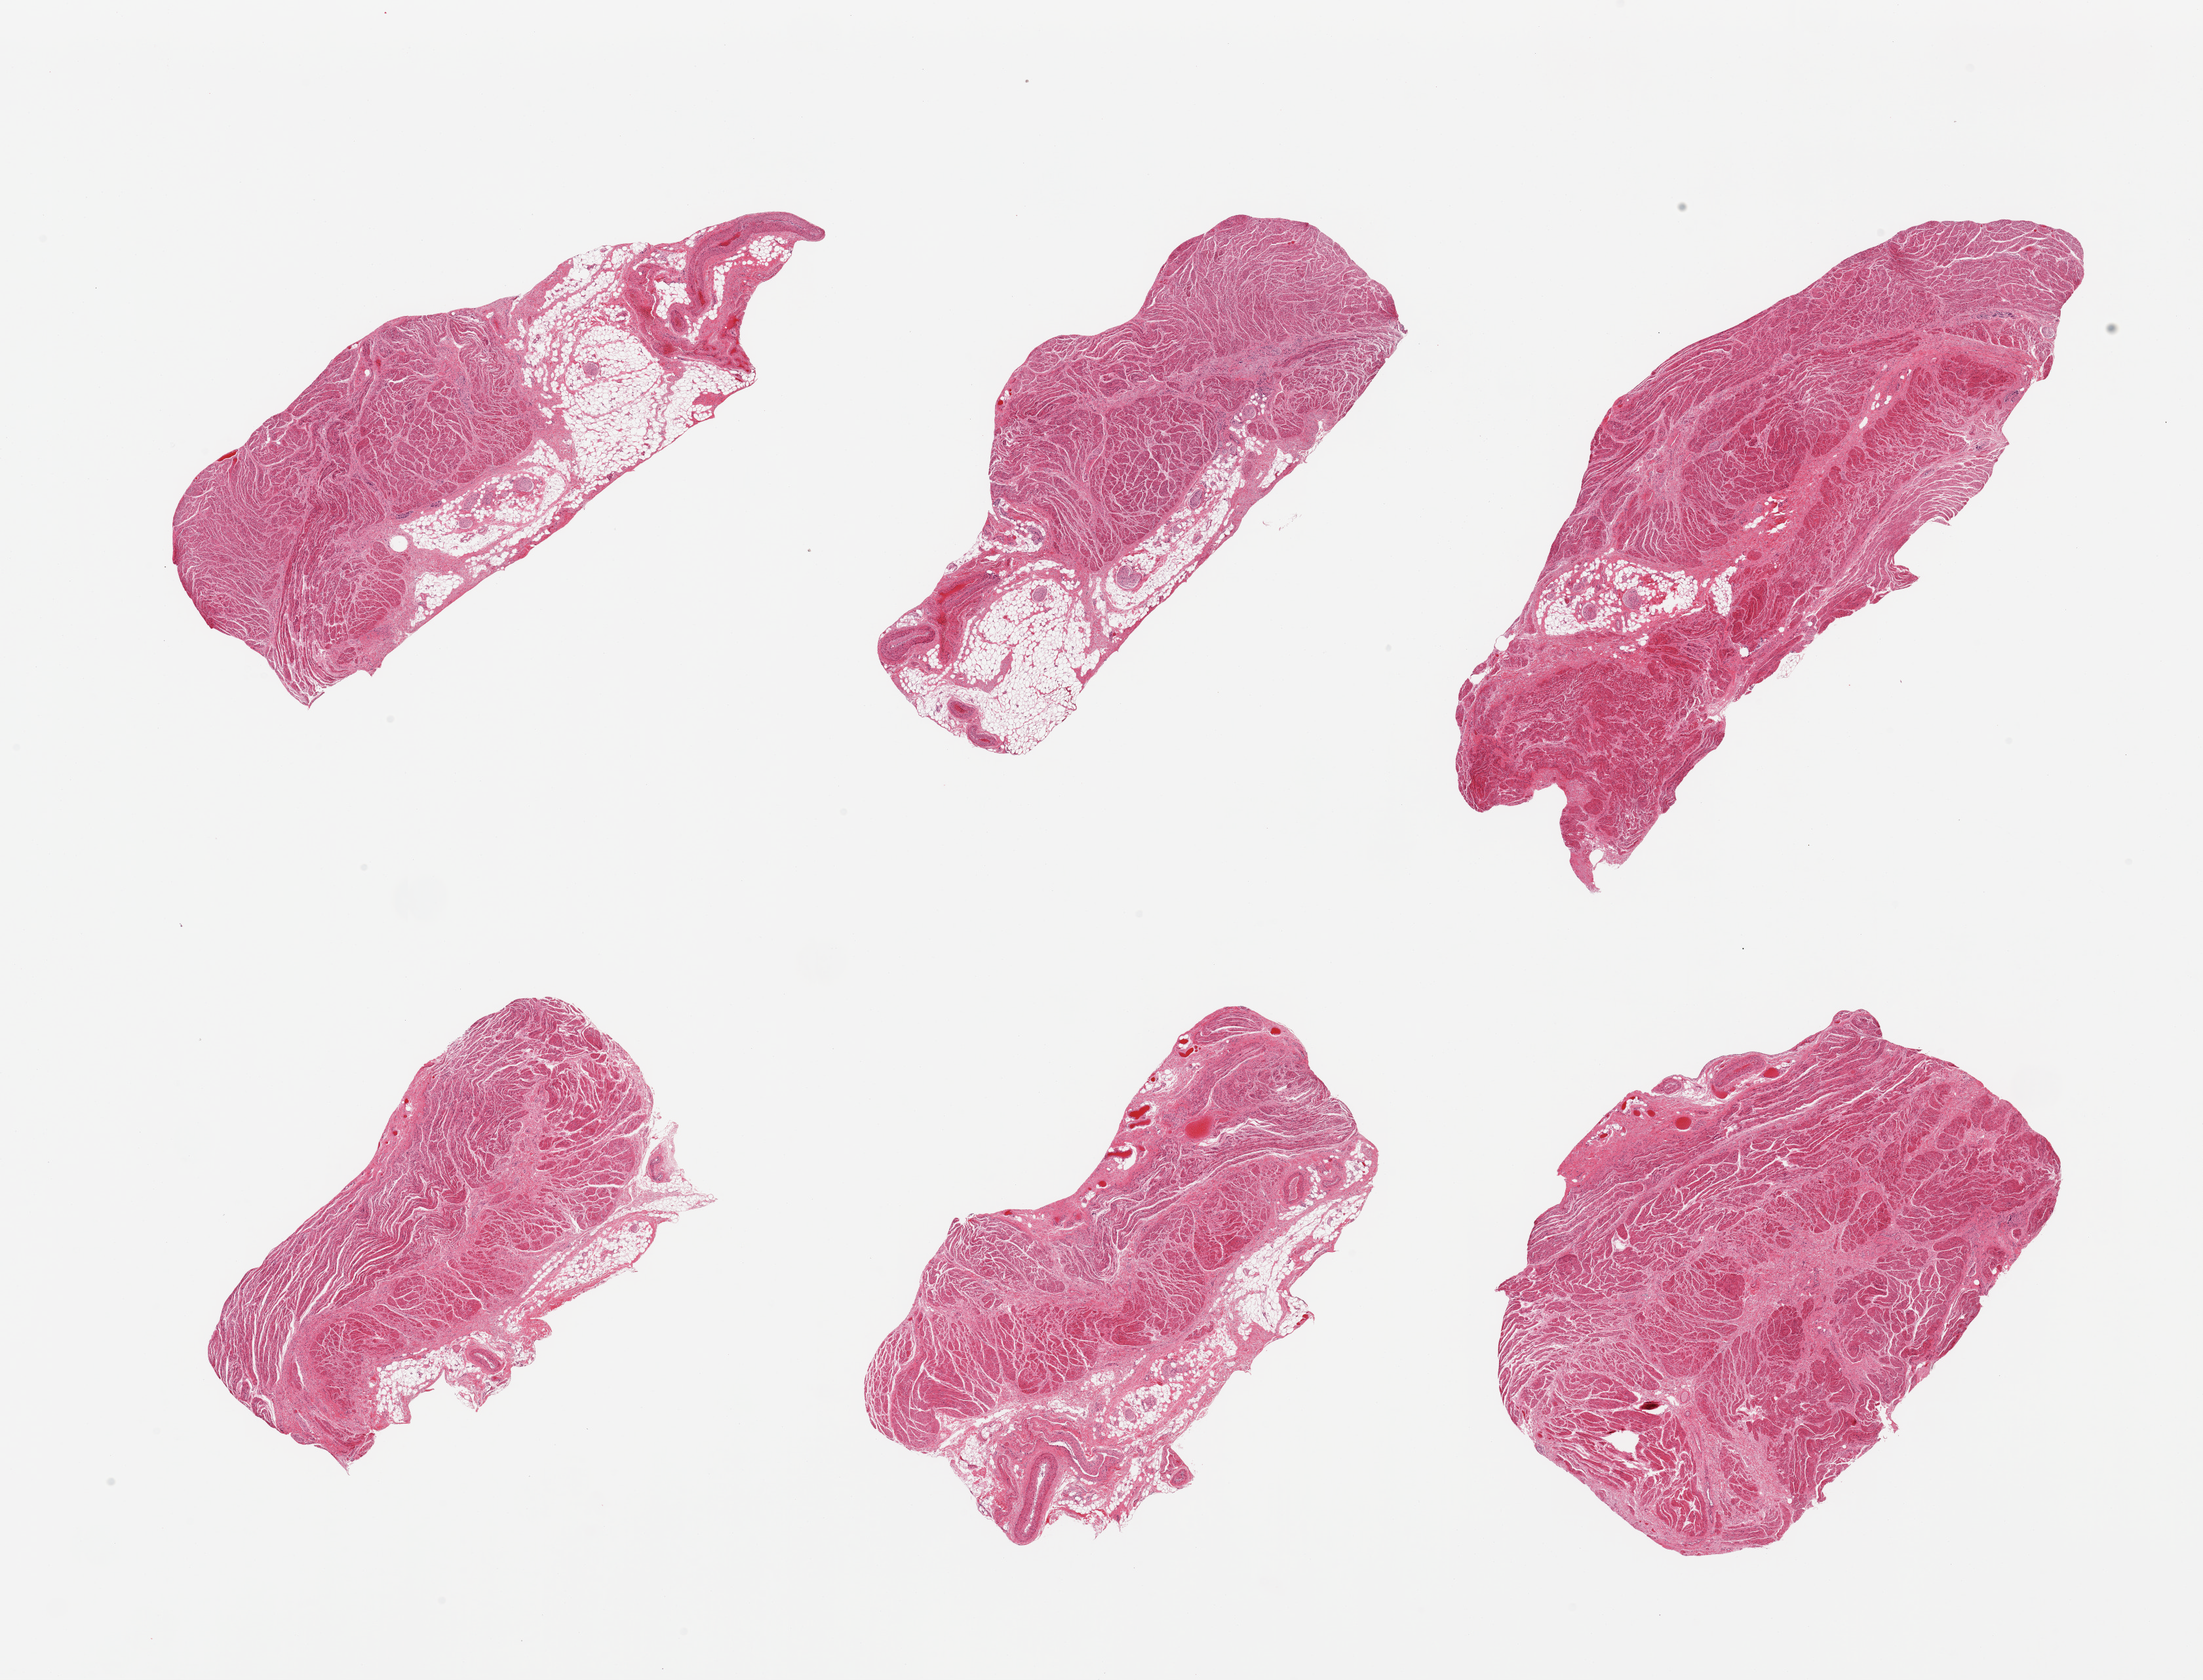
Hematoxylin and eosin (H&E) whole-slide image — shown as a low-resolution overview of the whole scanned area (about 26.6 x 20.3 mm); PAXgene-fixed, paraffin-embedded tissue; section of gastroesophageal junction (target tissue); tissue donor sample. Male donor.
• reviewer comment on this tissue sample: 6 pieces; 5 - 25% internal/external fat